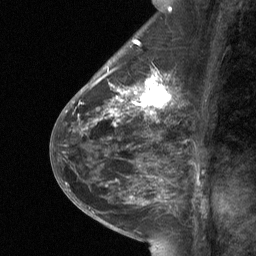
Breast MRI (dynamic contrast-enhanced), one sagittal slice. Position 25 of 64 along the scan axis. Dynamic contrast-enhanced study with each time point stored as its own series, time point 2 of 3 at this slice position (early post-contrast, ordered by acquisition time). 1.5 T. TE 4.8 ms, TR 27 ms. 2 mm slice thickness. 256 × 256 image matrix, field of view 180 × 180 mm. Female patient, age 59 years. From the clinical record (not read from this slice): setting: breast cancer imaged before/during neoadjuvant chemotherapy; receptor status: triple-negative.
Annotated regions visible in this slice (semi-automatic segmentation, software-assisted and operator-edited):
- analysis volume of interest (the breast-tissue region the enhancement analysis was run in; not a lesion): bounding box [x1, y1, x2, y2] px = [113, 66, 175, 120]
- tumour enhancement mask (voxels above the 90 % enhancement threshold inside the analysis volume of interest): [113, 69, 173, 115]